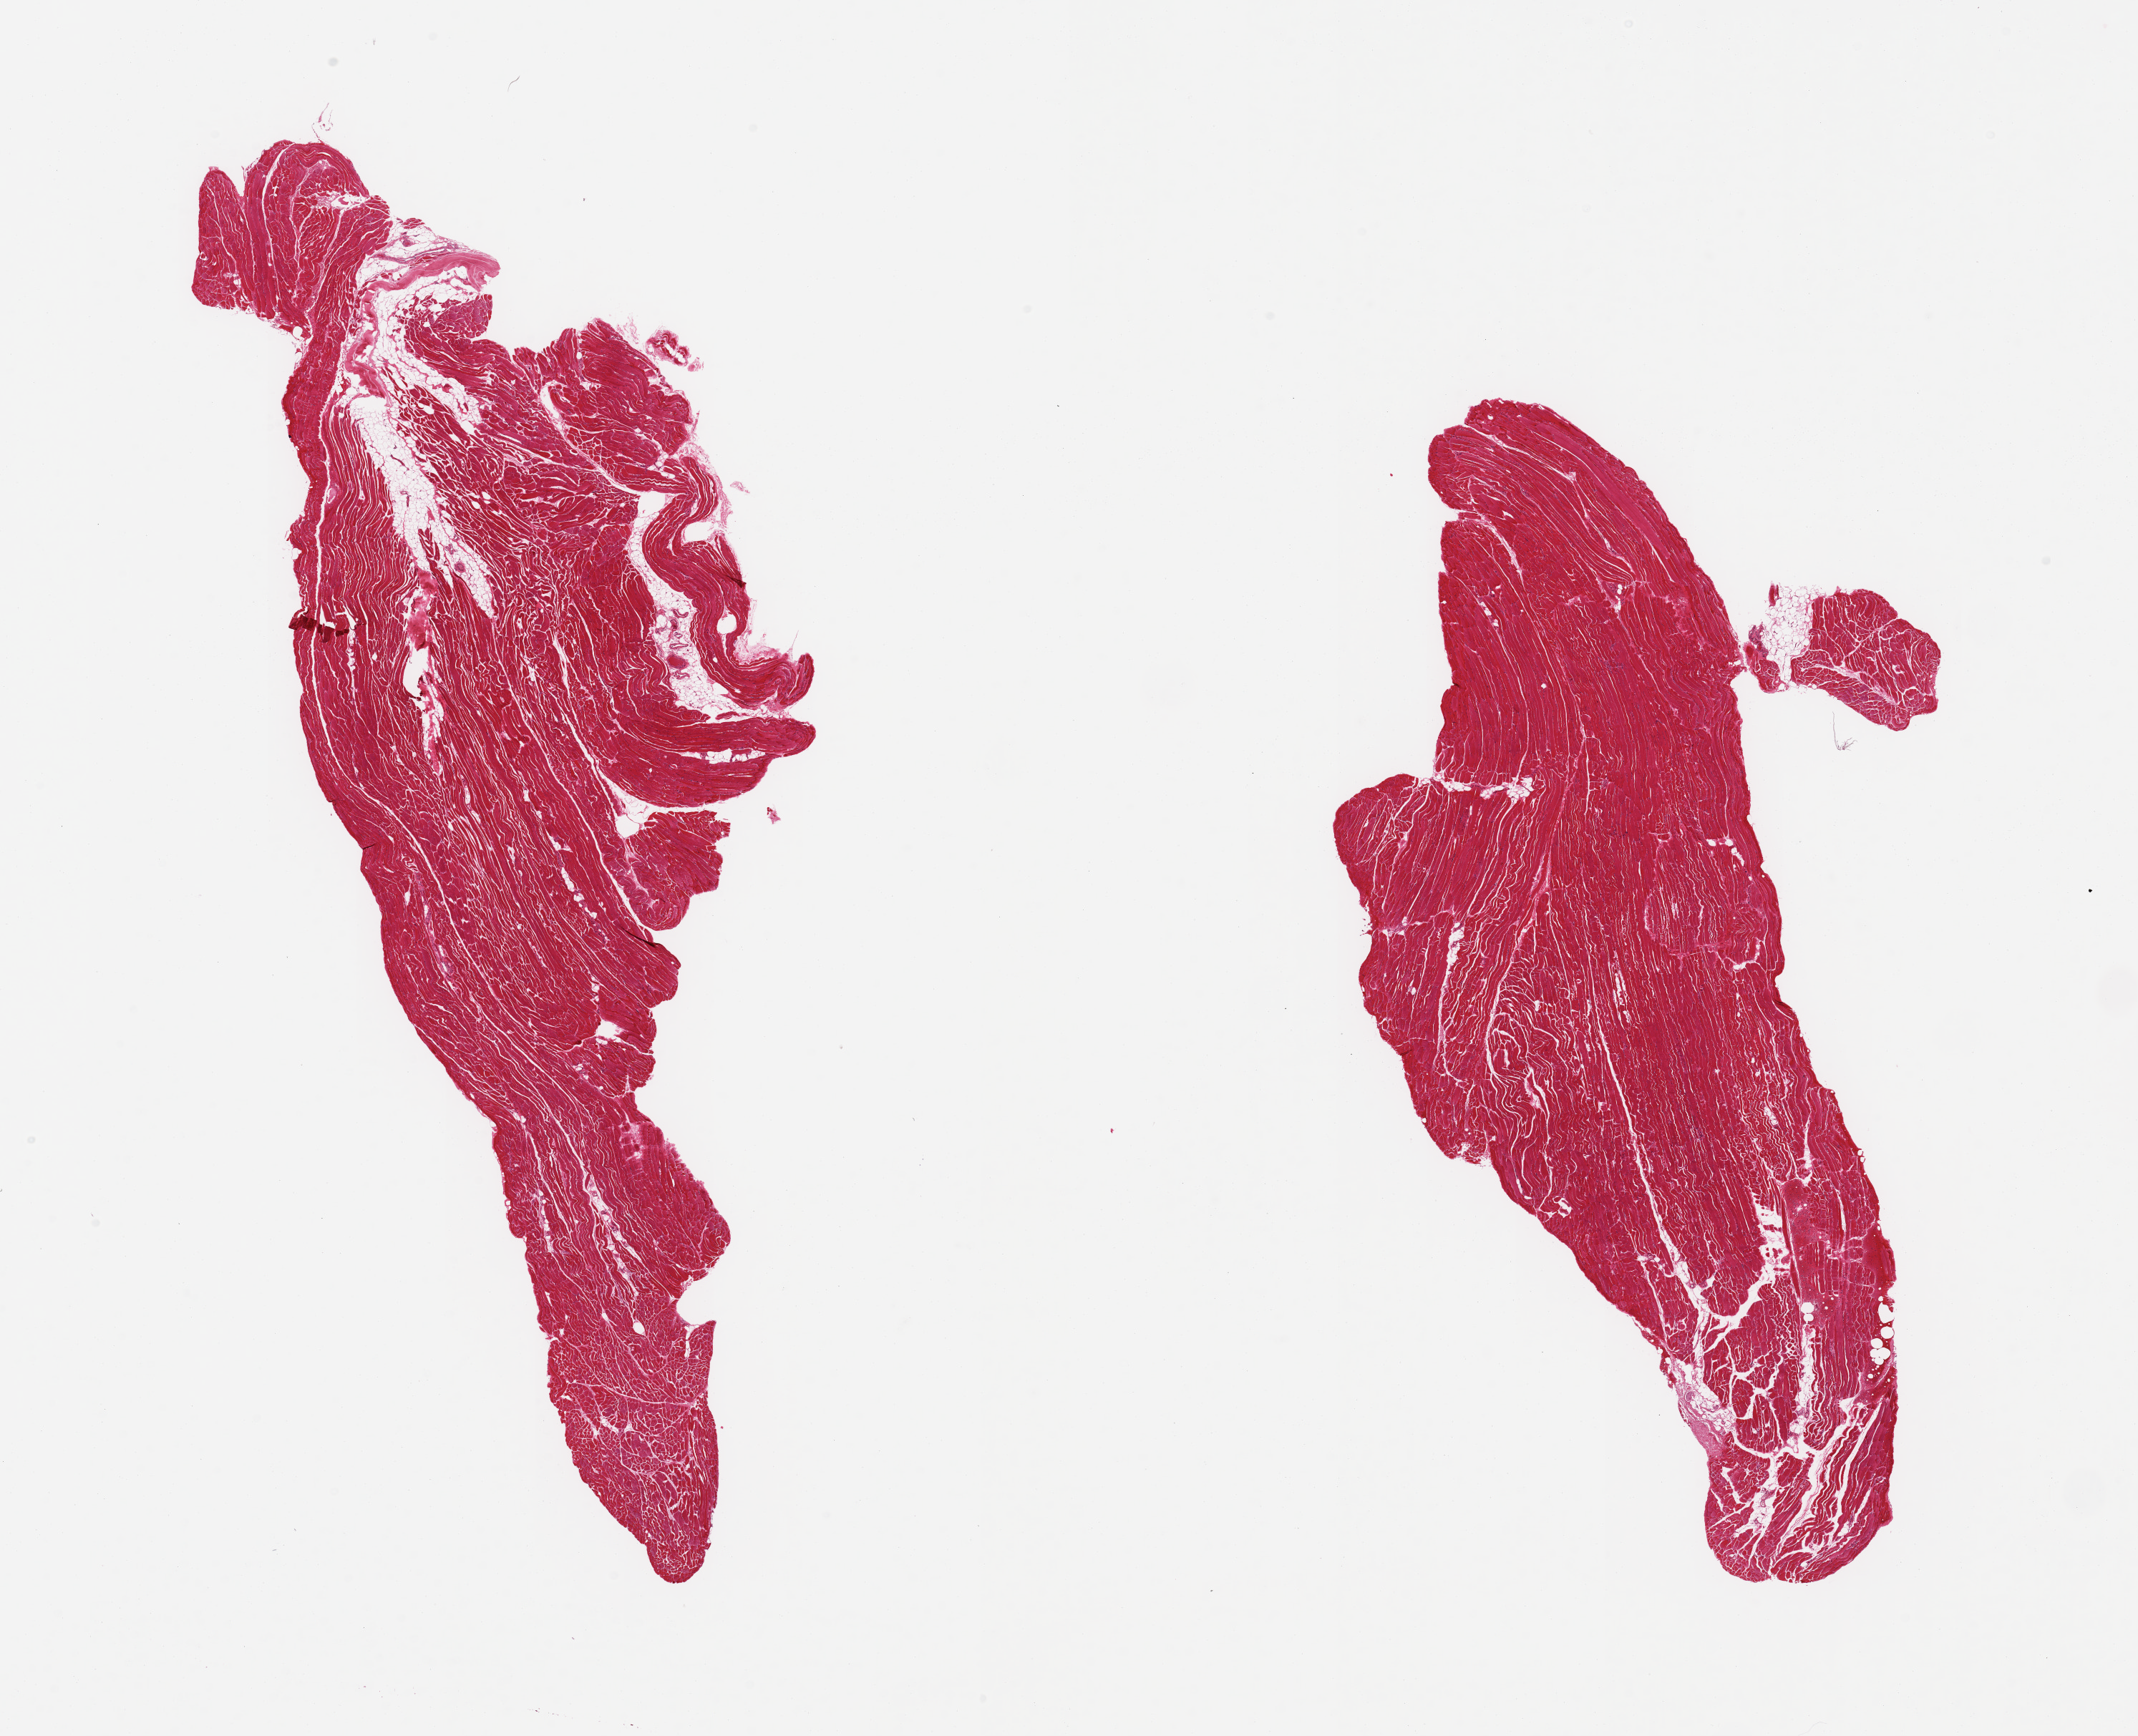
Digitized hematoxylin and eosin (H&E)-stained section, shown as a low-resolution overview of the whole scanned area (about 23.6 x 19.2 mm, slide scanned at 20x), PAXgene-fixed, paraffin-embedded tissue, section of skeletal muscle (target tissue), donor tissue sample. Female donor.
Reviewer comment on this tissue sample: 2 pieces, ~5% interstitial fat.